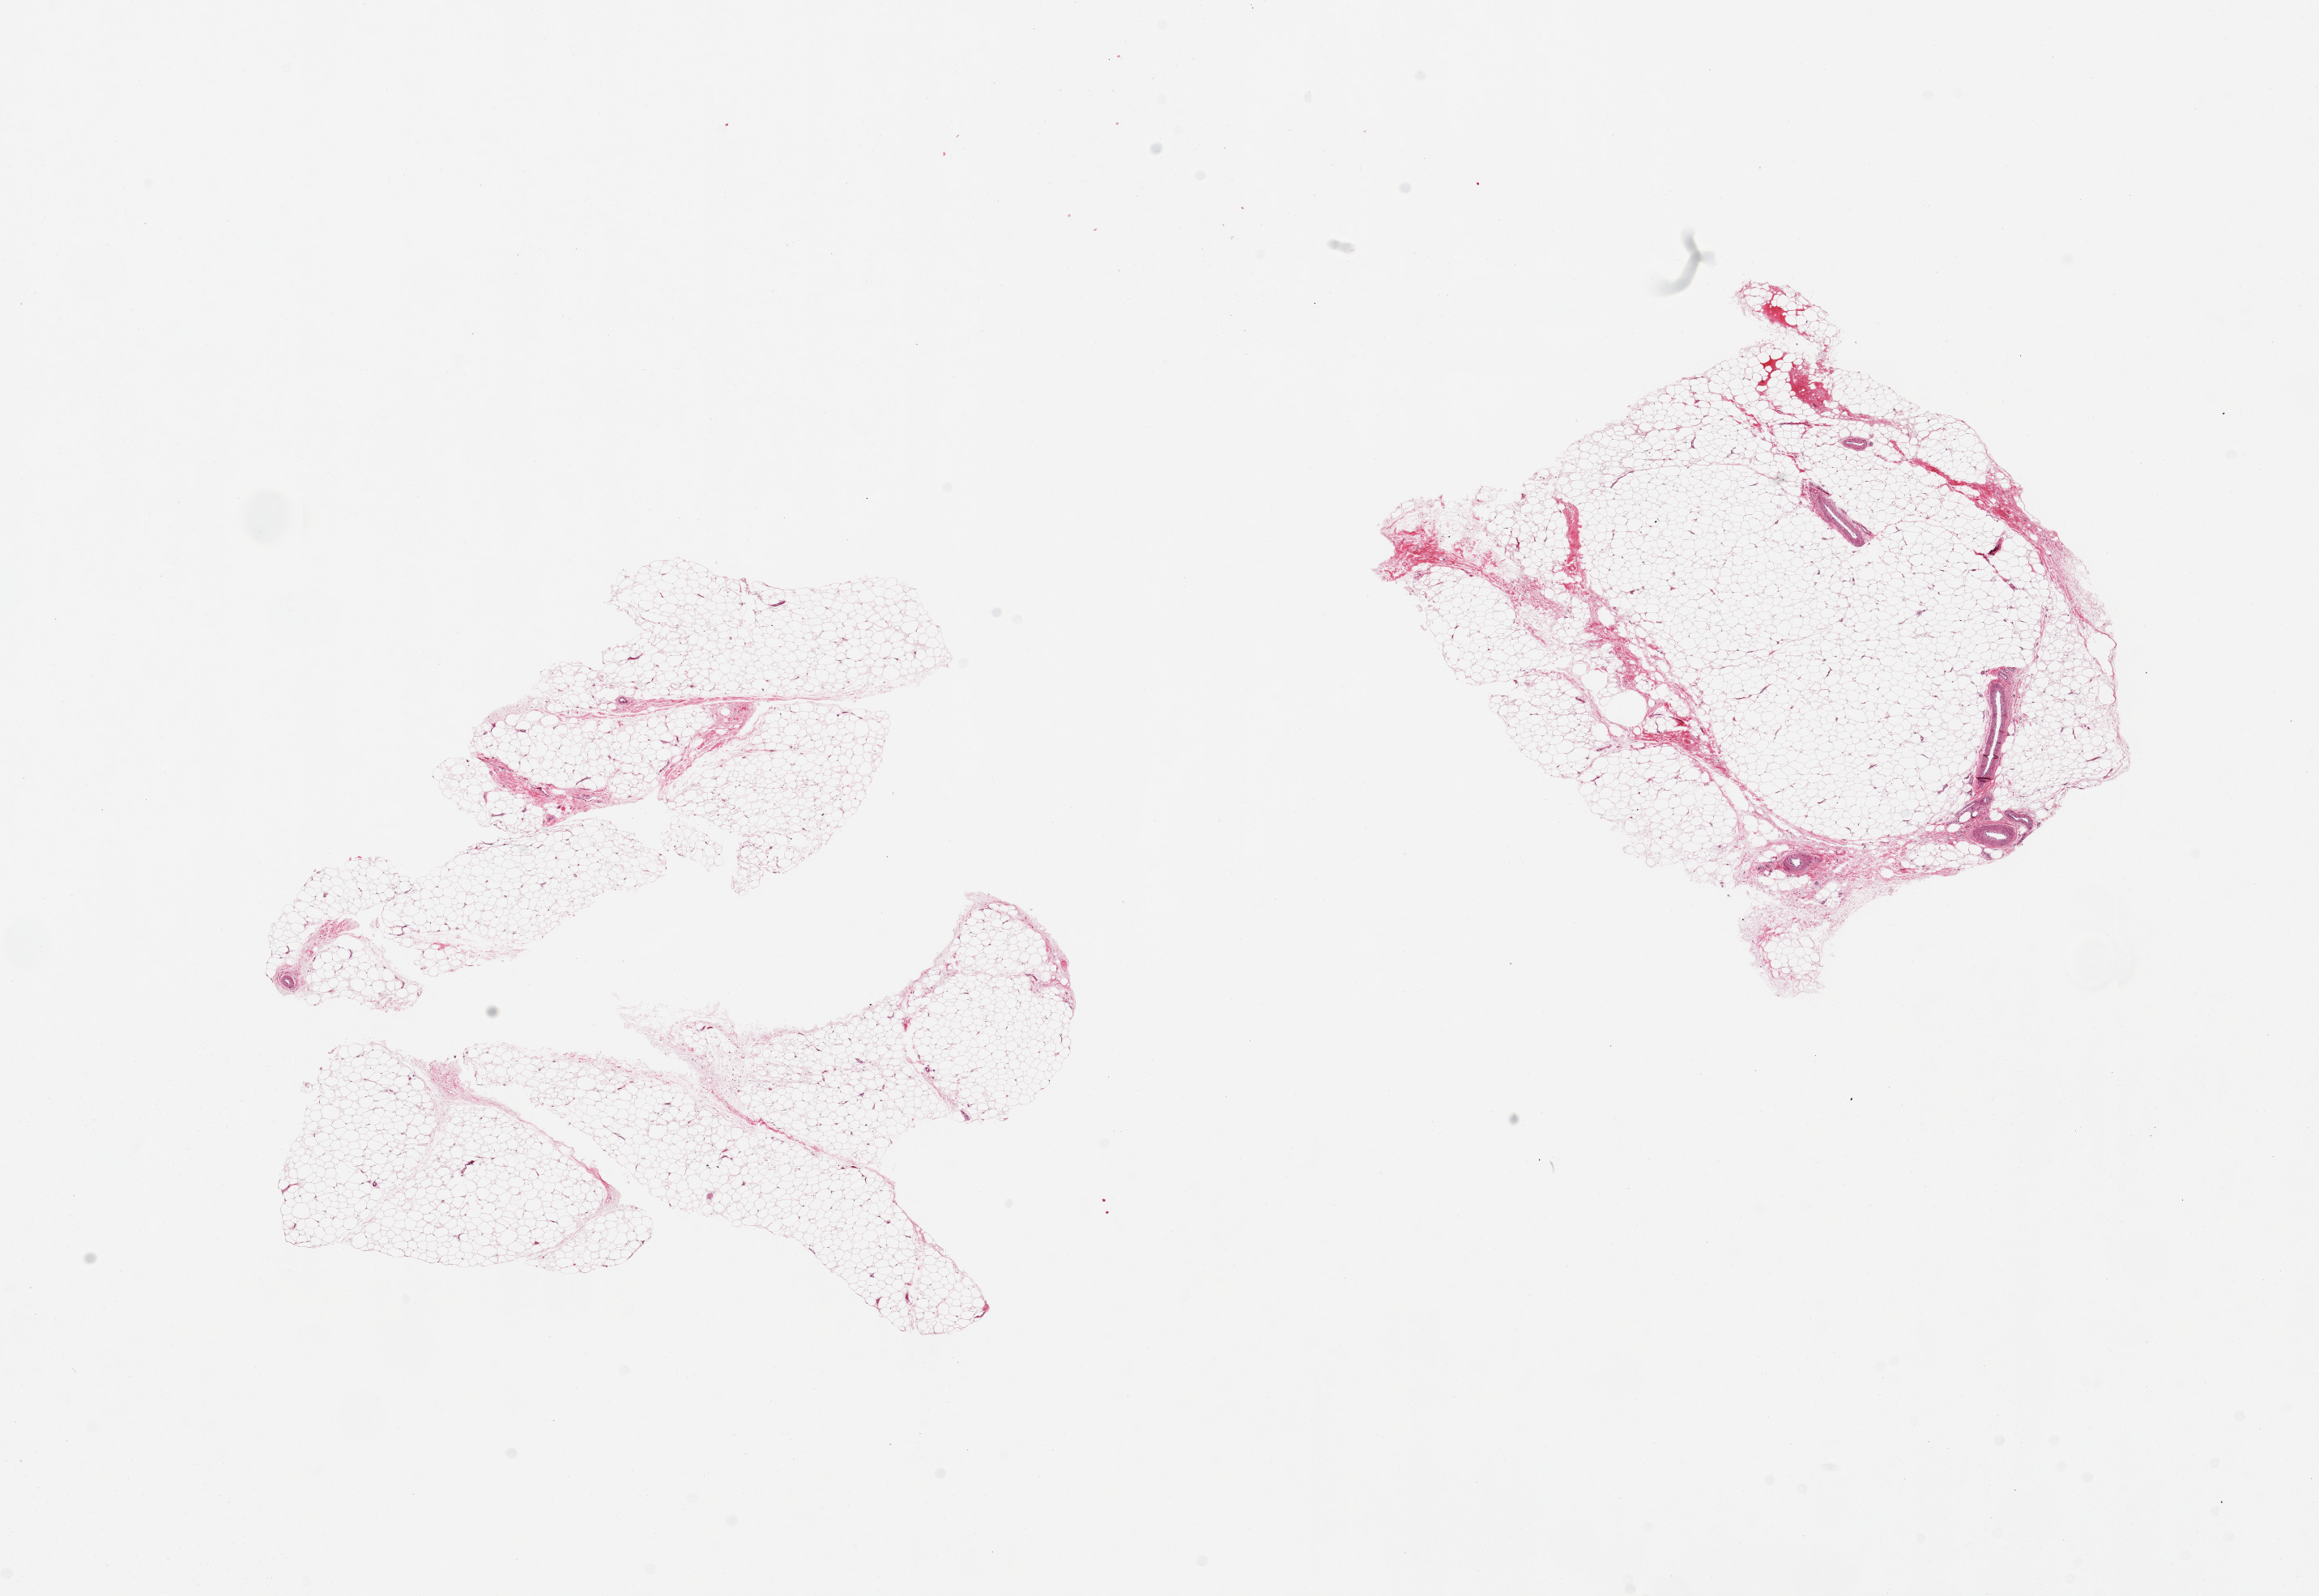
Digitized H&E-stained section, shown as a low-resolution overview of the whole scanned area (about 22.6 x 15.6 mm). PAXgene-fixed paraffin-embedded (PFPE) section. Target tissue: adipose tissue. Tissue donor sample. Male donor.
Reviewer comment on this tissue sample: 2 pieces; 10% fibrovascular component.